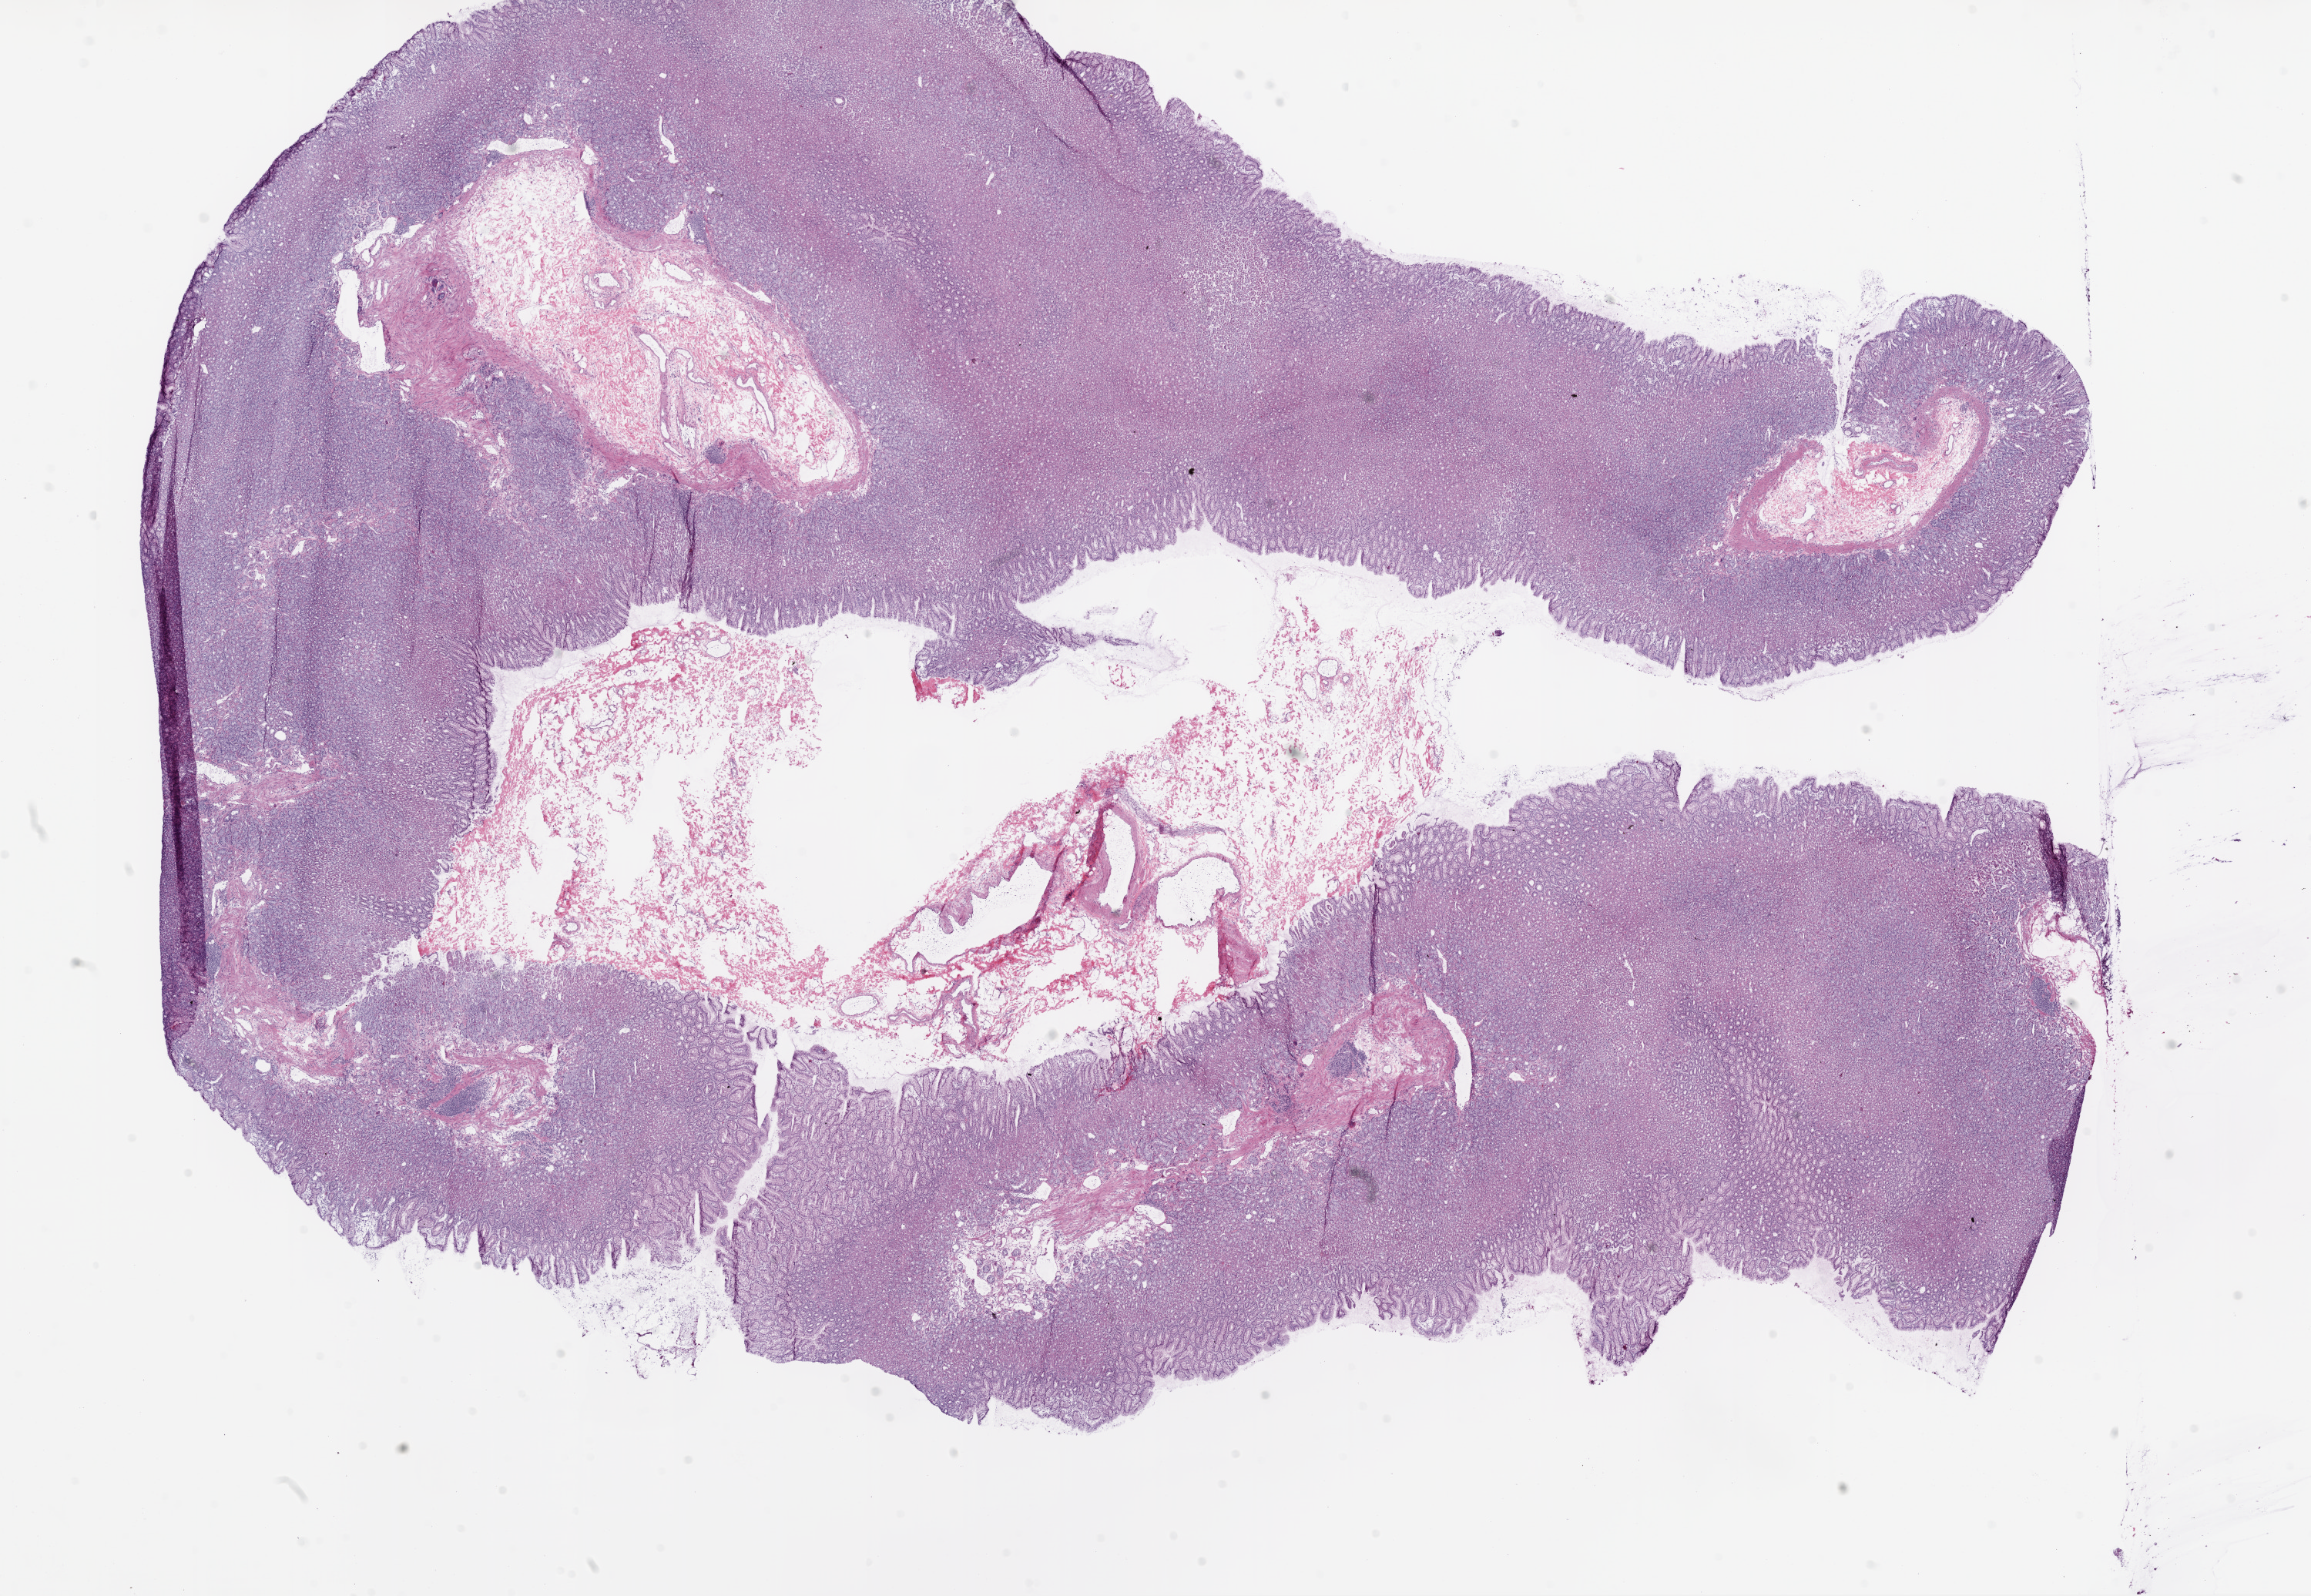
Digitized Hematoxylin and eosin (H&E) stained tissue section (whole slide), low-resolution overview of the scanned area, about 24.1 x 16.6 mm (from a 20x scan); frozen section from the top of the tissue portion; stomach, solid tissue normal (non-tumour tissue) sample. Patient: male, age at initial diagnosis 58 years.
This section: solid tissue normal sample (biorepository sample class). Patient diagnosis: Adenocarcinoma, NOS (body of stomach).